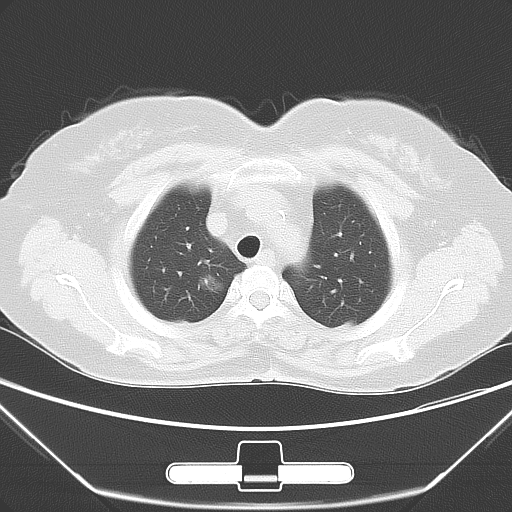
Chest CT, one axial slice; slice 46 of 55 in the series (ordered by position); 120 kVp; lung window (W 1500 / L -600 HU); 5 mm slice thickness; 512 × 512 image matrix, field of view 356 × 356 mm. Female patient, age 63 years. Case-level facts recorded for this patient, not image findings: clinical TNM (as recorded): T1a N0 M0.
Outlined on this slice (bounding box drawn by a radiologist):
- lung tumour (recorded histology: adenocarcinoma): bounding box [x1, y1, x2, y2] px = [184, 267, 229, 299]